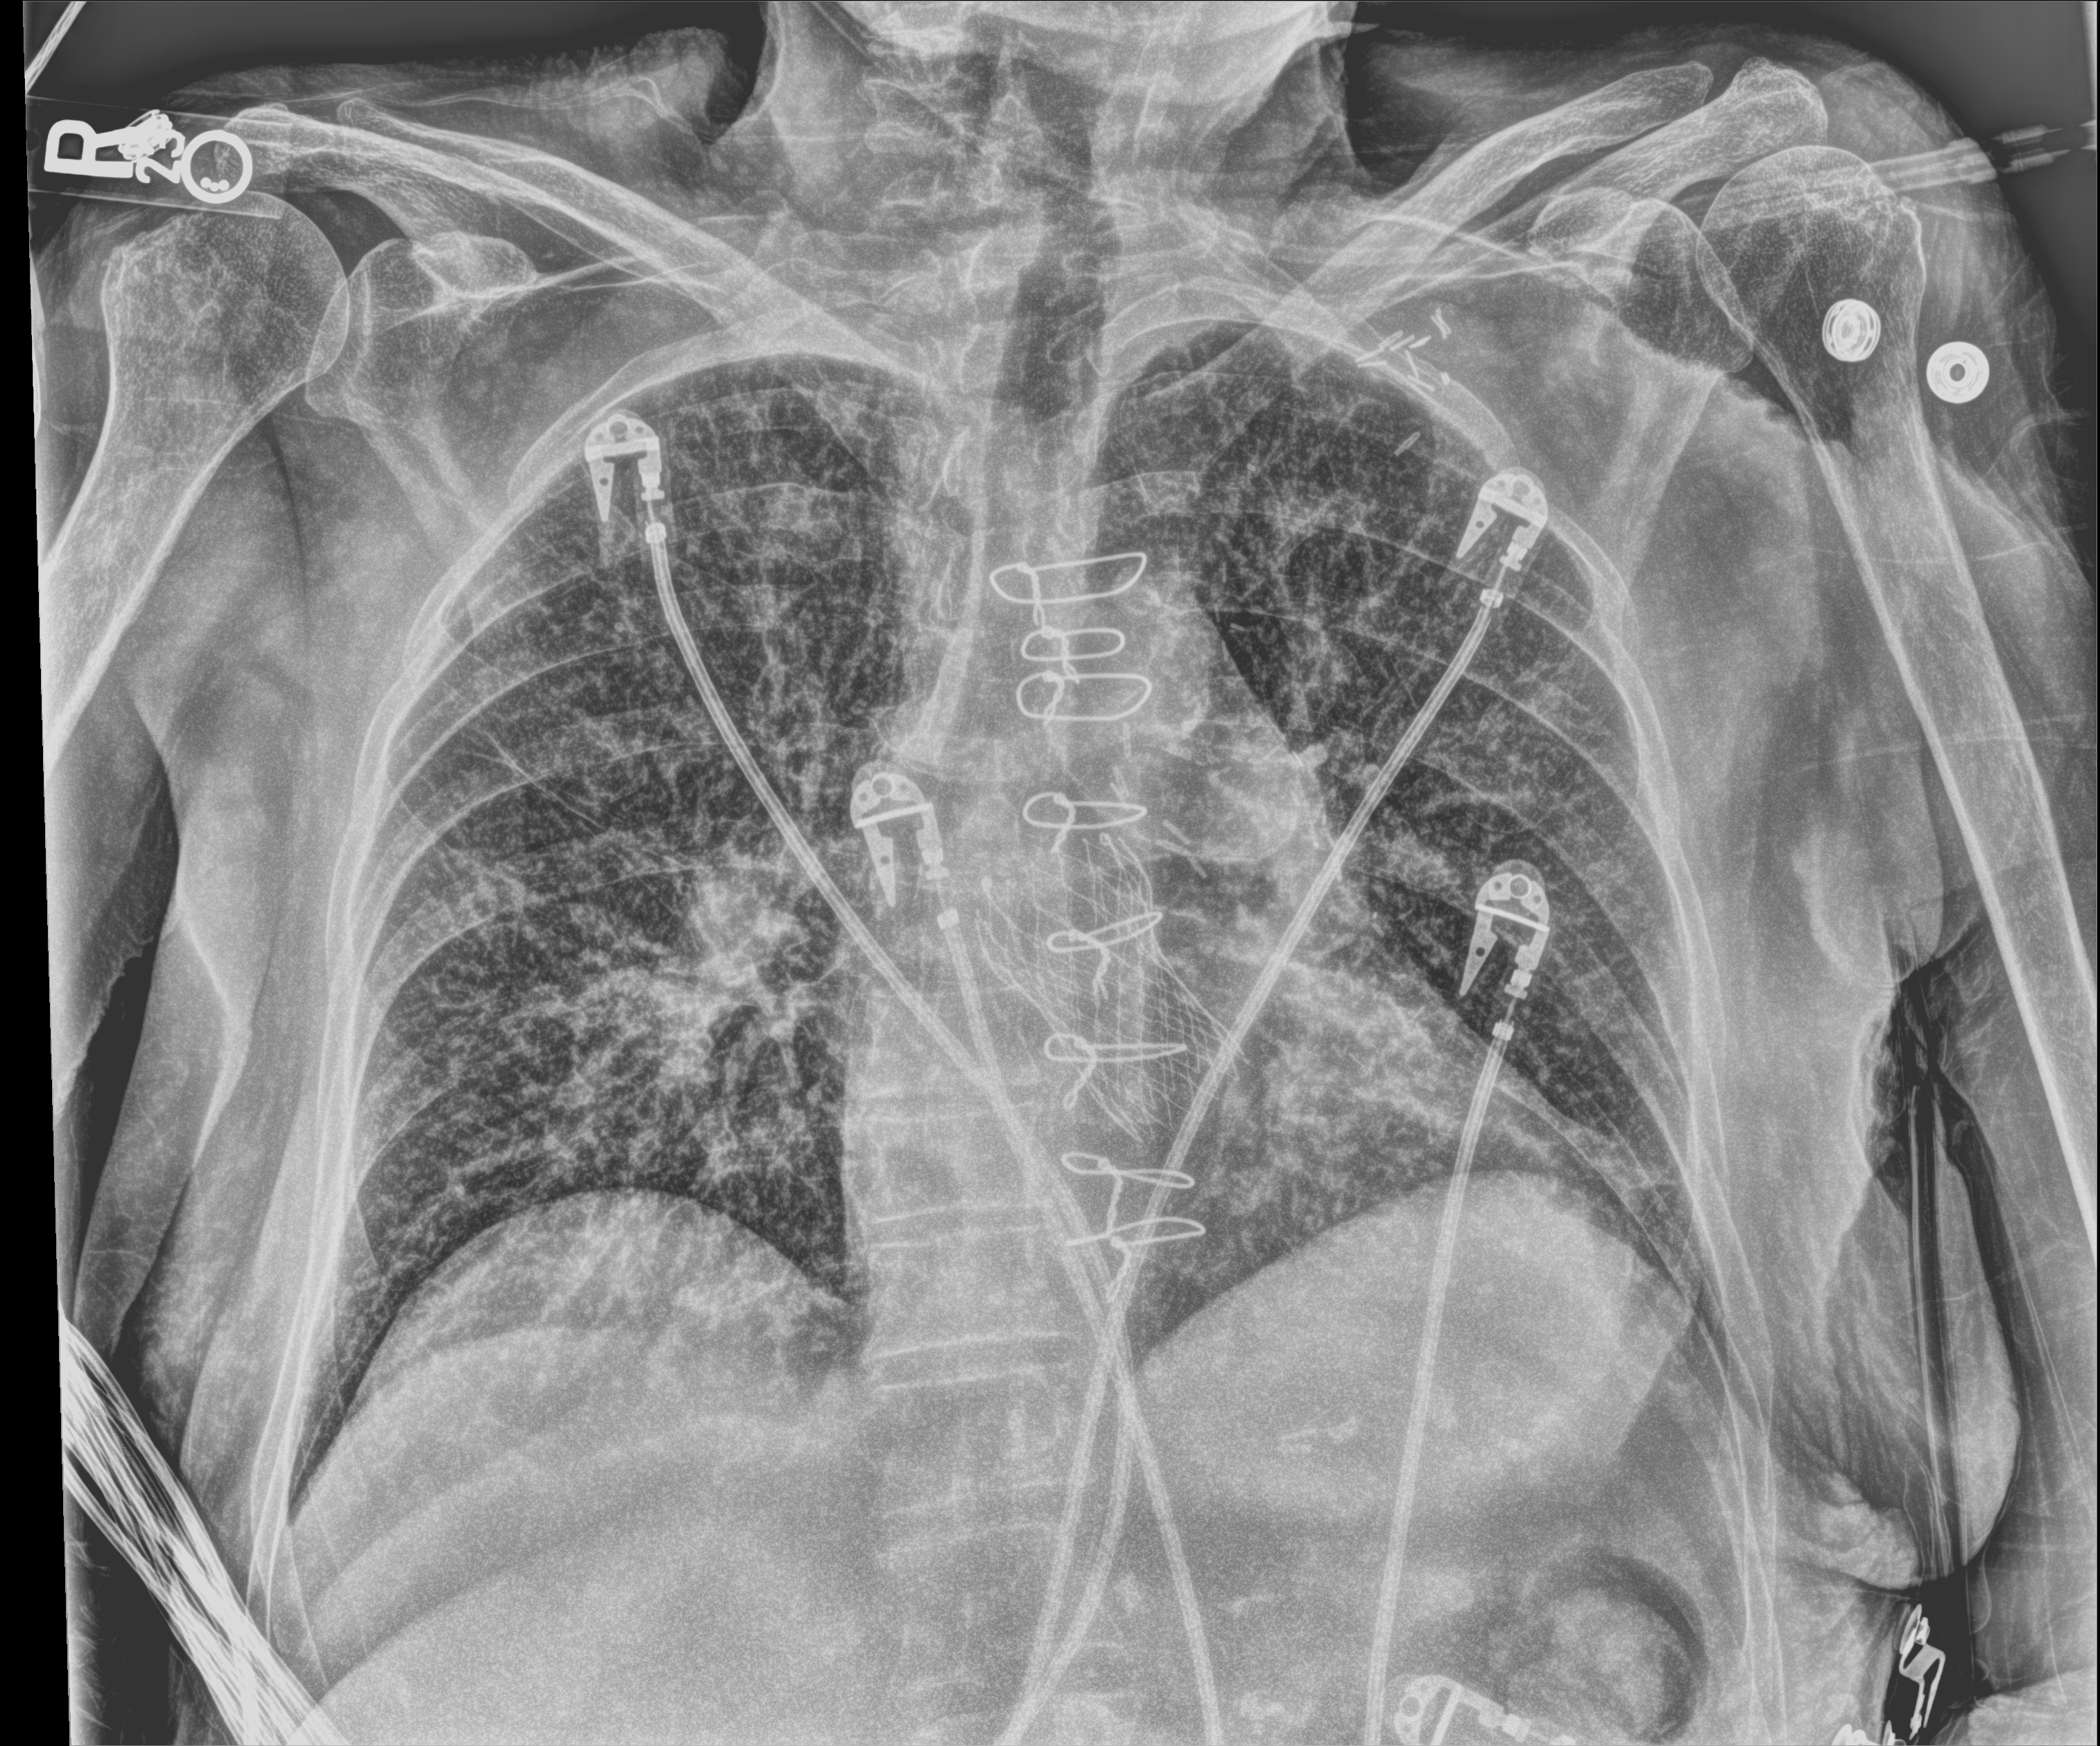
Portable chest radiograph. Patient hospitalised with COVID-19; female, aged 75–90 years.
From the hospital-stay record, not from the radiograph (when in the stay this image was taken is not recorded):
- admitted to intensive care during this hospital stay: yes